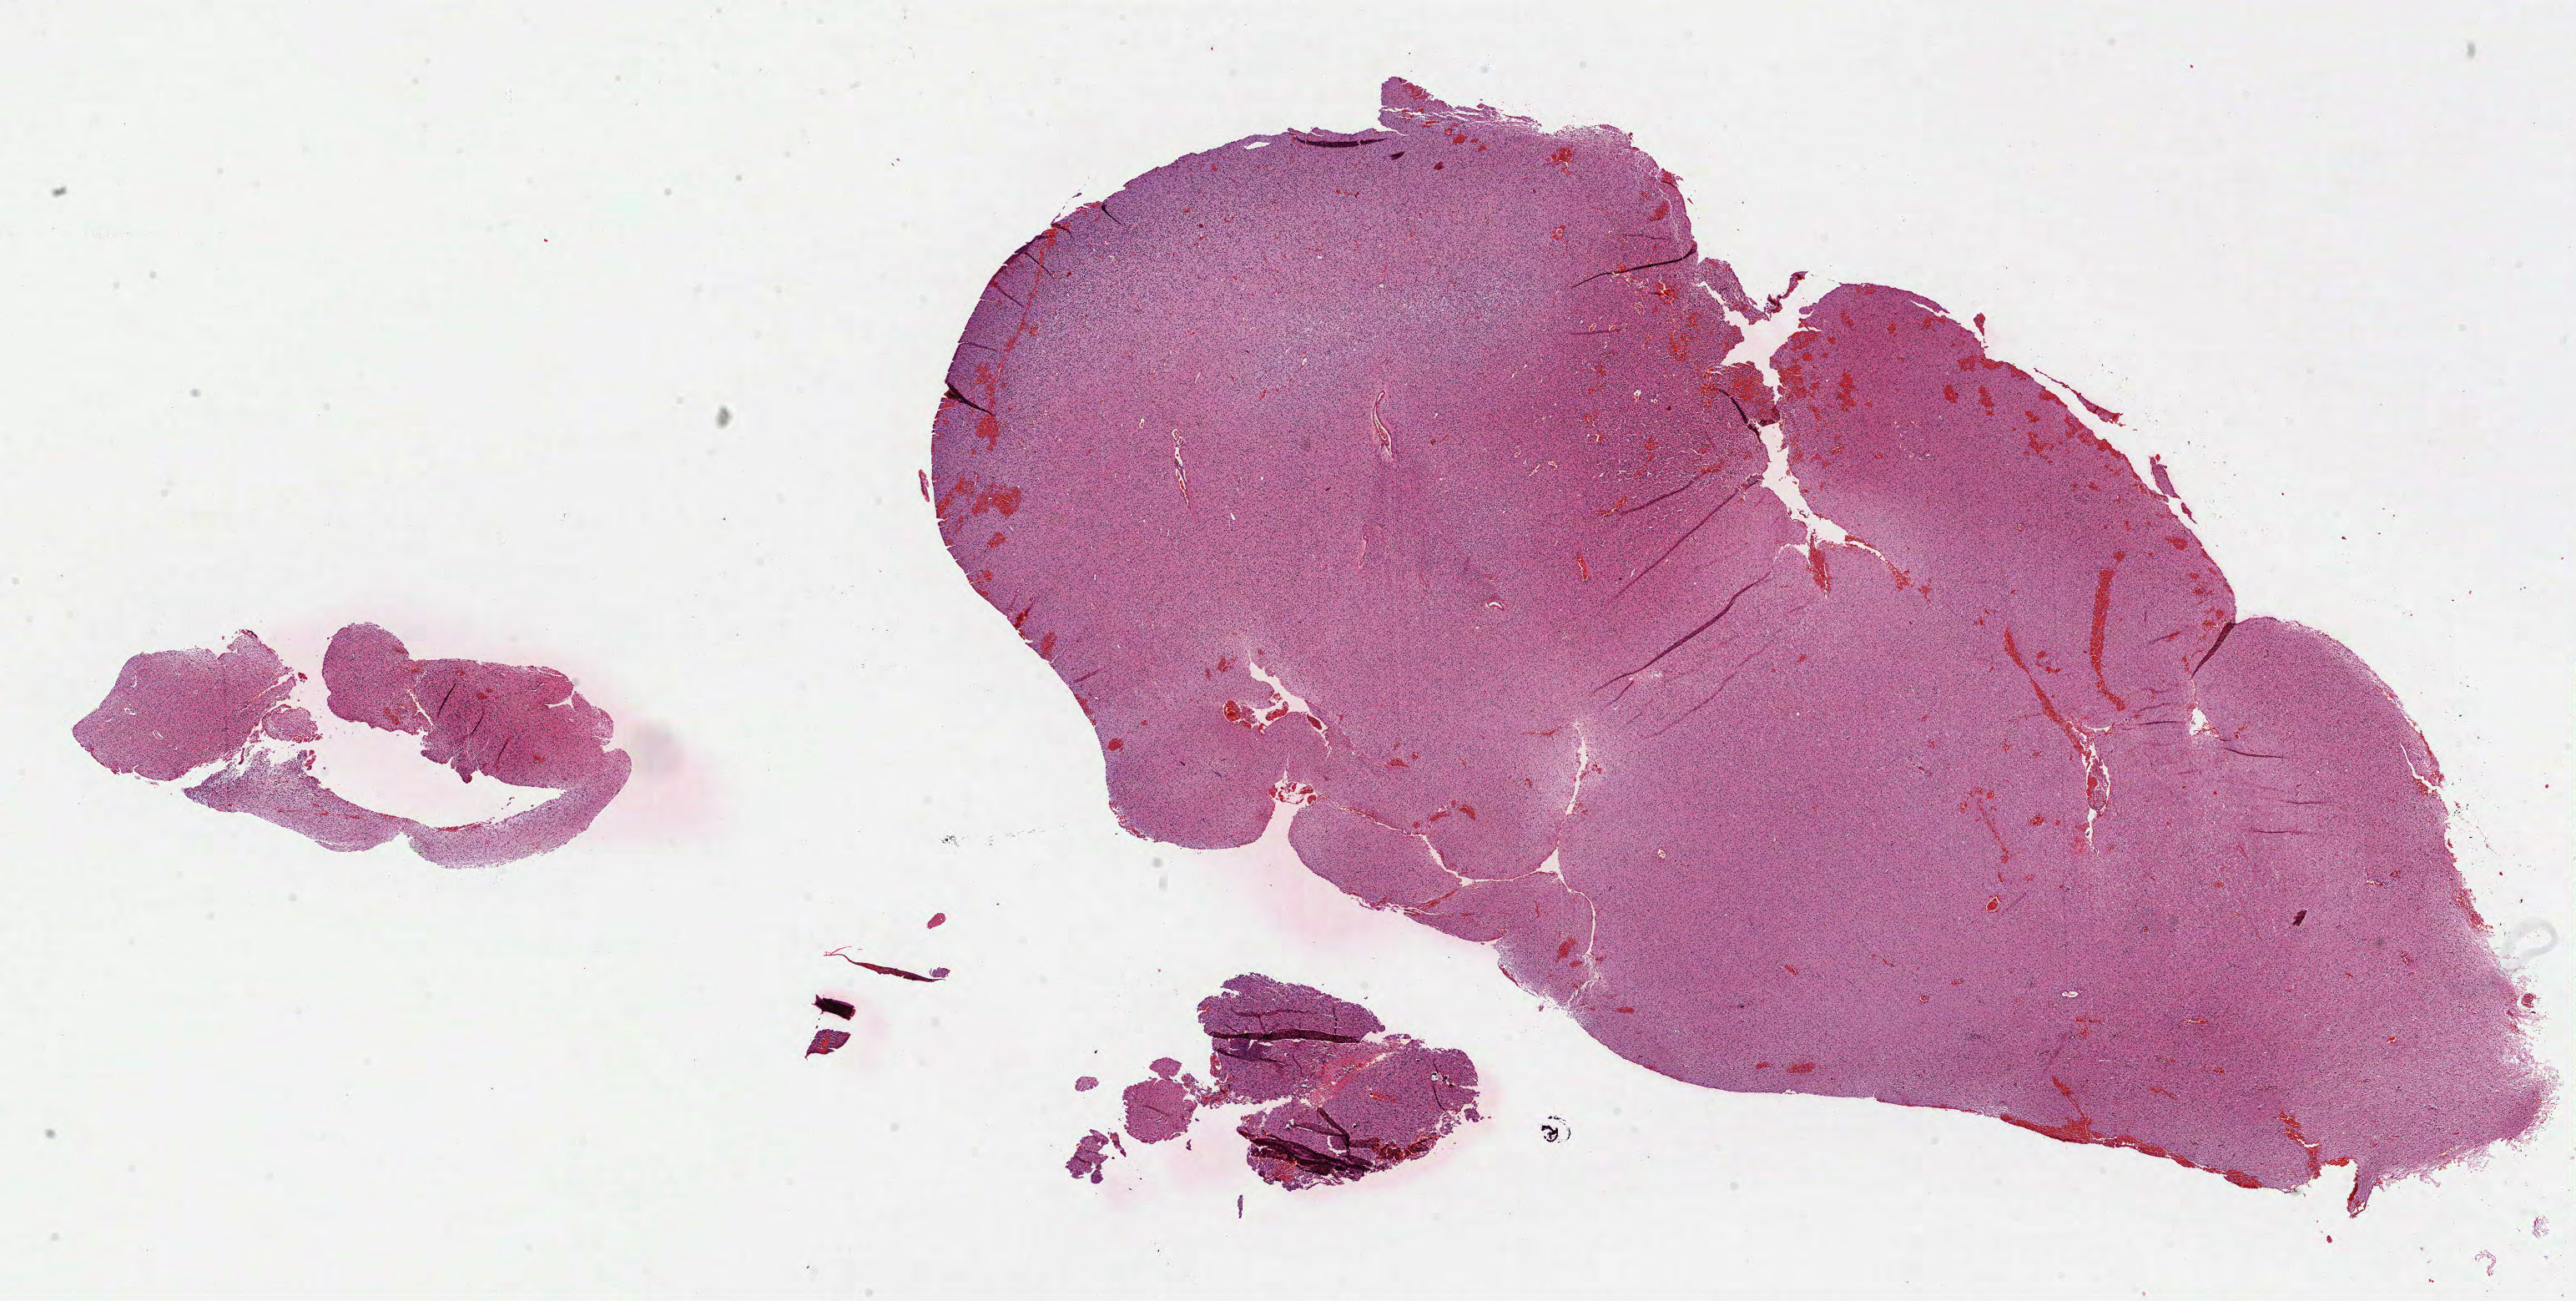
H&E whole-slide image, a low-resolution overview of the entire scanned area, about 24.9 x 12.6 mm (from a 40x scan), FFPE section, brain, primary tumour sample. Male patient; age at initial diagnosis 39 years. Histologic grade: G3 (poorly differentiated).
Diagnosis: Astrocytoma, anaplastic.